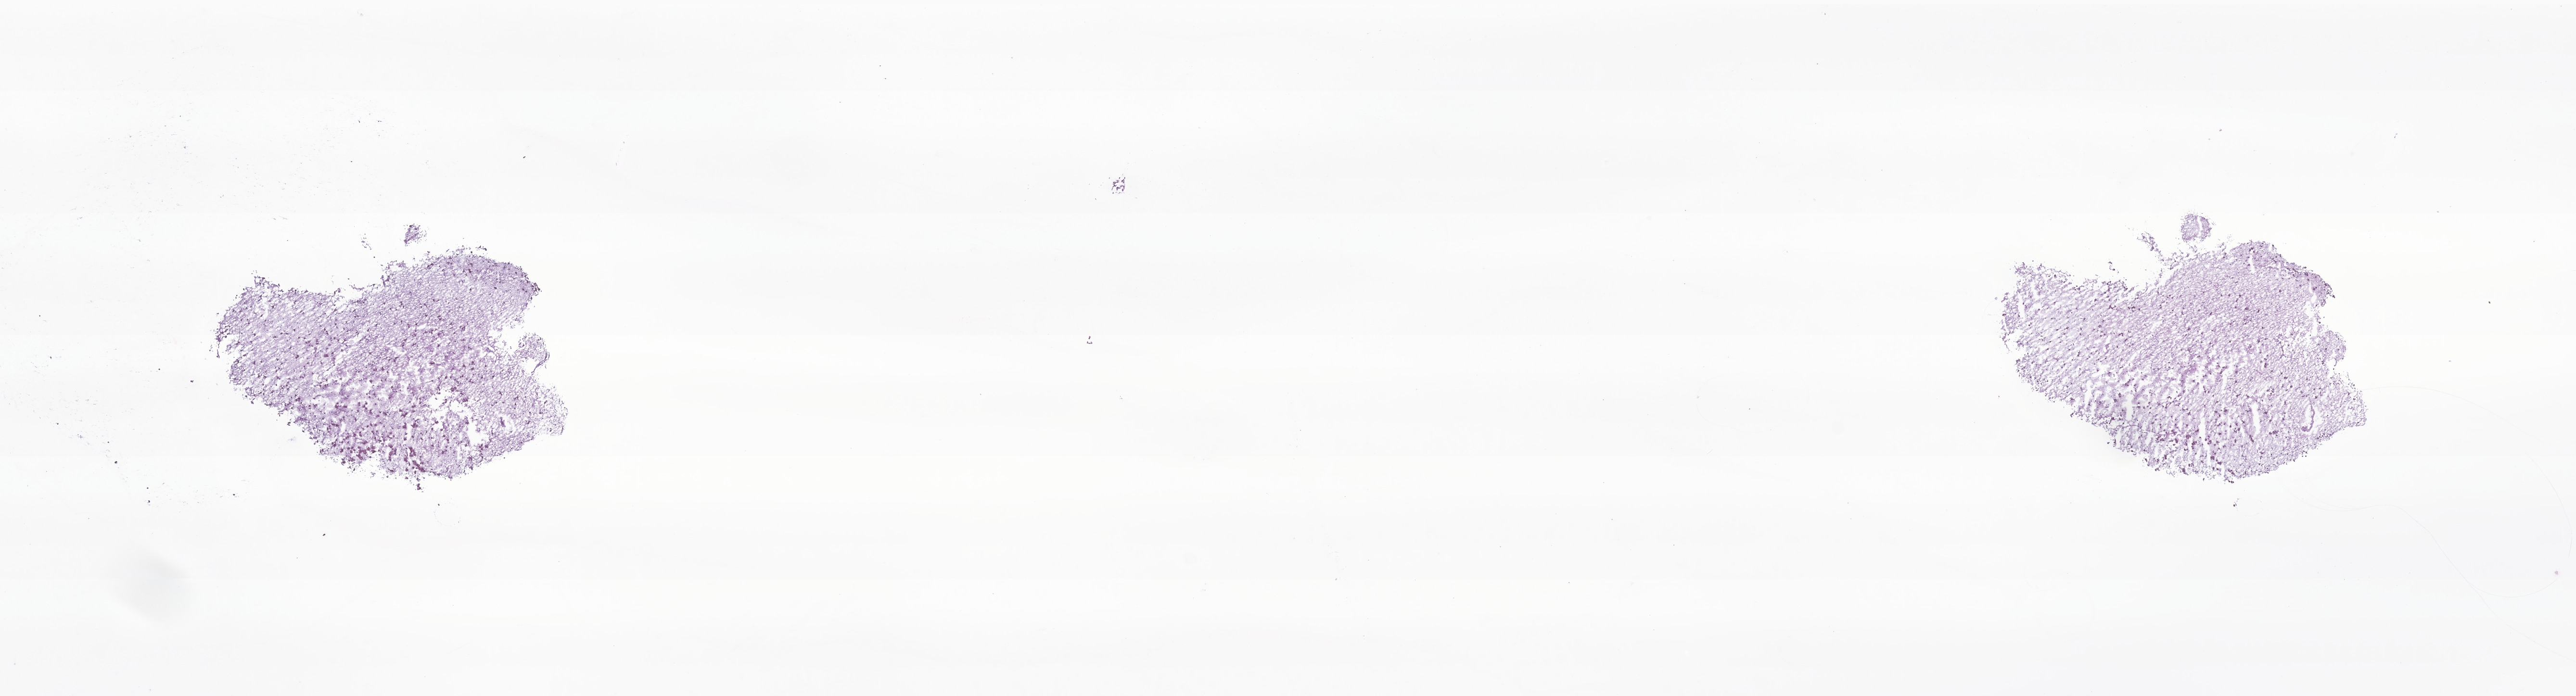
Haematoxylin and eosin whole-slide image of tumor tissue from the brain, a low-resolution overview of the entire scanned area, about 22.6 x 6.1 mm. Cryosection (OCT / tissue freezing medium). Male patient, age 184 months.
* diagnosis (ICD-O-3 morphology term): Ganglioglioma, NOS